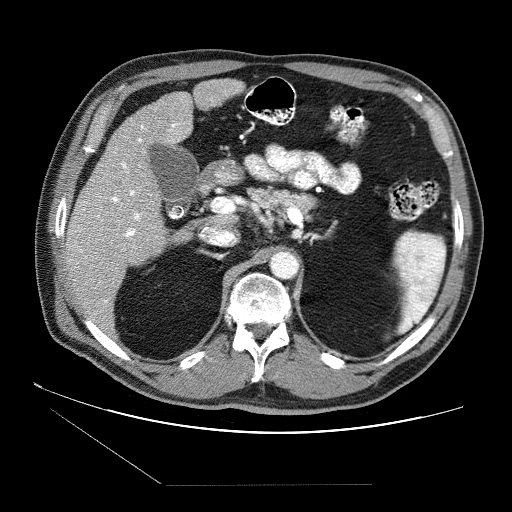
Contrast-enhanced abdominal CT (liver protocol), one axial slice. Reconstruction kernel STANDARD. 120 kVp. Soft-tissue window (W 400 / L 40 HU). 512 × 512 image matrix, field of view 400 × 400 mm. From the clinical record (not read from this slice): diagnosis: hepatocellular carcinoma (patient treated with transarterial chemoembolisation; whether this scan precedes or follows treatment is not stated here); TNM stage (as recorded): Stage-II; Child-Pugh class: B; tumour differentiation: no biopsy; tumour size: 2.6 cm.
Structures marked on this image (semi-automatic segmentation, software-assisted and operator-edited):
- liver parenchyma outside the tumour (the mass and vessels are separate outlines, so this box may not span the whole liver): bounding box [x1, y1, x2, y2] px = [65, 78, 244, 328]
- liver vessels: [73, 123, 184, 315]